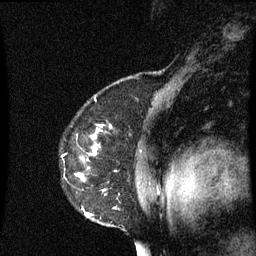
Breast MRI (dynamic contrast-enhanced), one sagittal slice; position 52 of 60 along the scan axis; dynamic contrast-enhanced series, image 2 of 3 at this slice position (ordered by acquisition); 1.5 T; TE 4.2 ms, TR 8.9 ms; 2 mm slice thickness; 256 × 256 image matrix. Female patient, age 53 years. From the clinical record (not read from this slice): setting: breast cancer imaged before/during neoadjuvant chemotherapy; receptor status: HR-positive, HER2-negative.
Structures marked on this image (semi-automatically segmented with operator editing):
- analysis volume of interest (the breast-tissue region the enhancement analysis was run in; not a lesion): bounding box <64,130,155,227> (left, top, right, bottom; pixels)
- tumour enhancement mask (voxels above the 70 % enhancement threshold inside the analysis volume of interest): <76,136,97,217>